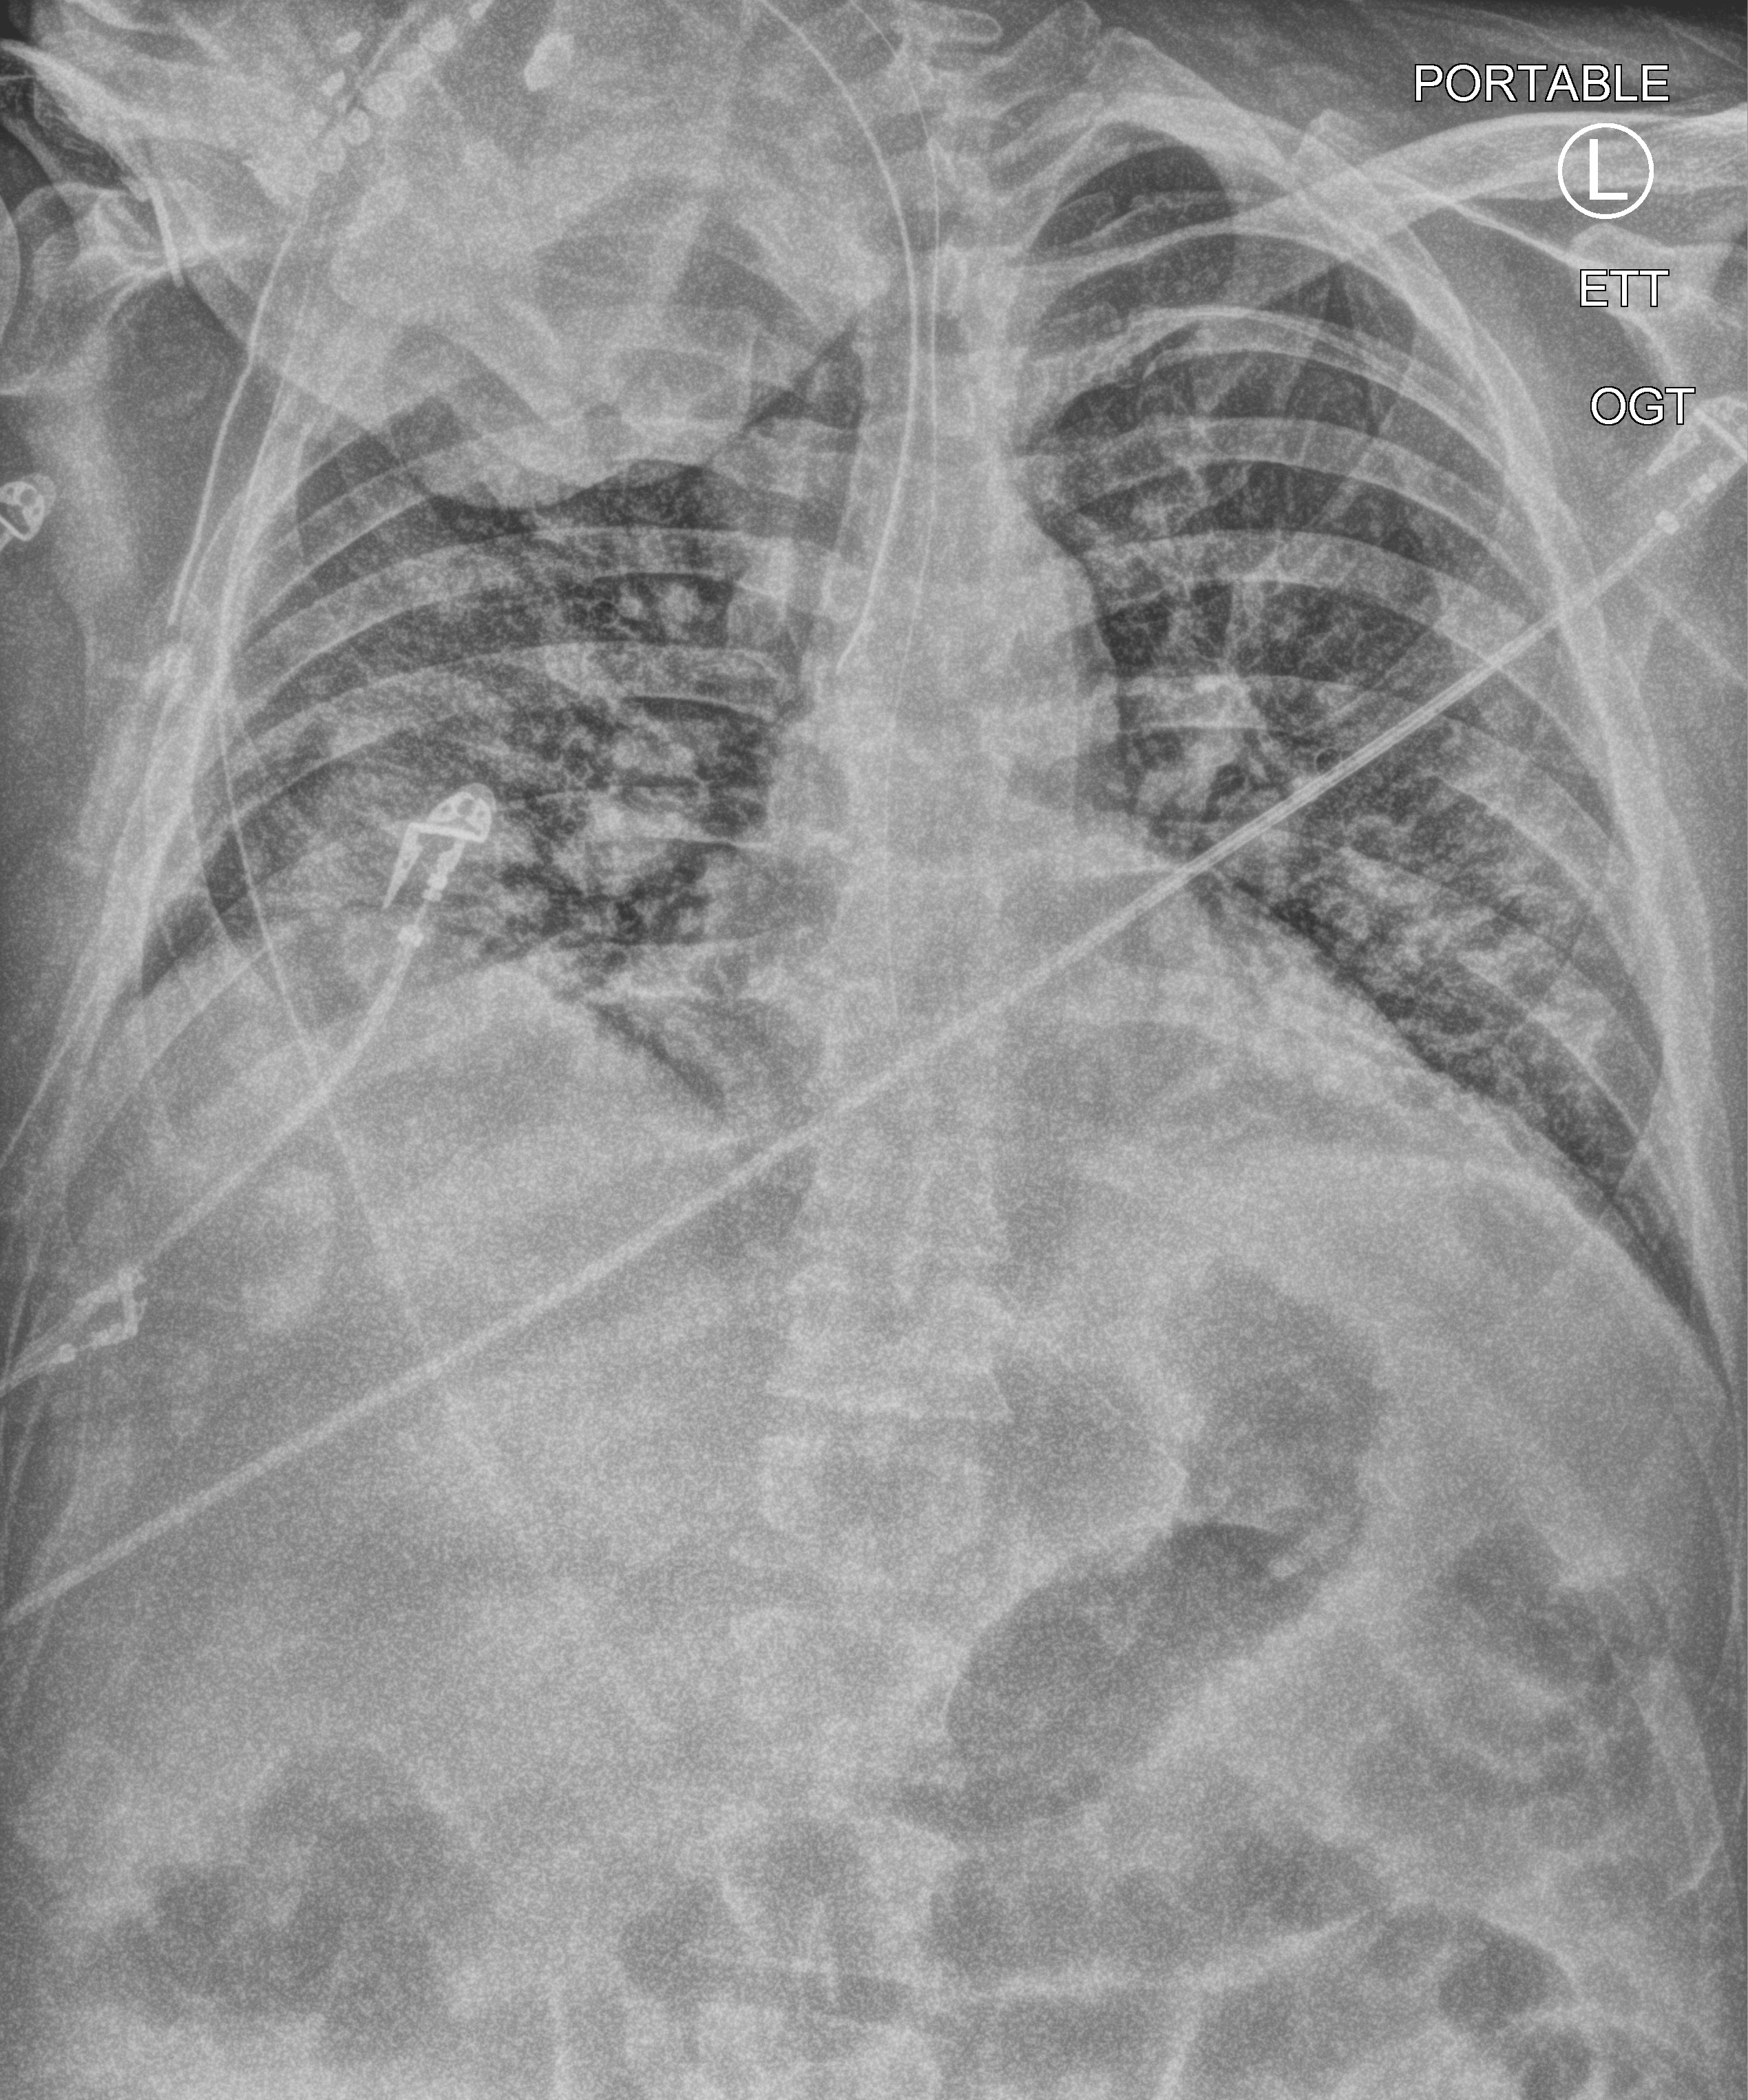
Portable chest radiograph. Patient hospitalised with COVID-19; male, aged 18–59 years.
Hospital-stay facts (about this admission, not read from this image; timing relative to this image not recorded): mechanically ventilated during this hospital stay: yes; admitted to intensive care during this hospital stay: yes; diabetes (admission record): no.